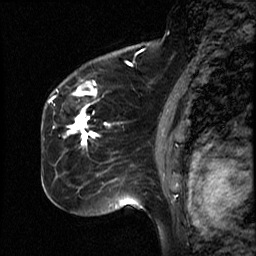
Breast MRI (dynamic contrast-enhanced), one sagittal slice. Slice 34 of 50 in the series (ordered by position). Dynamic contrast-enhanced study with each time point stored as its own series, time point 2 of 4 at this slice position (early post-contrast, ordered by acquisition time). 1.5 T. TE 4.2 ms, TR 18.5 ms. 256 × 256 image matrix, field of view 200 × 200 mm. Female patient, age 44 years. From the clinical record (not read from this slice): setting: breast cancer imaged before/during neoadjuvant chemotherapy; receptor status: HR-positive, HER2-negative.
Outlined on this slice (semi-automatically segmented with operator editing):
- analysis volume of interest (the breast-tissue region the enhancement analysis was run in; not a lesion): bounding box <59,80,114,206> (left, top, right, bottom; pixels)
- tumour enhancement mask (voxels above the 100 % enhancement threshold inside the analysis volume of interest): <67,105,98,146>